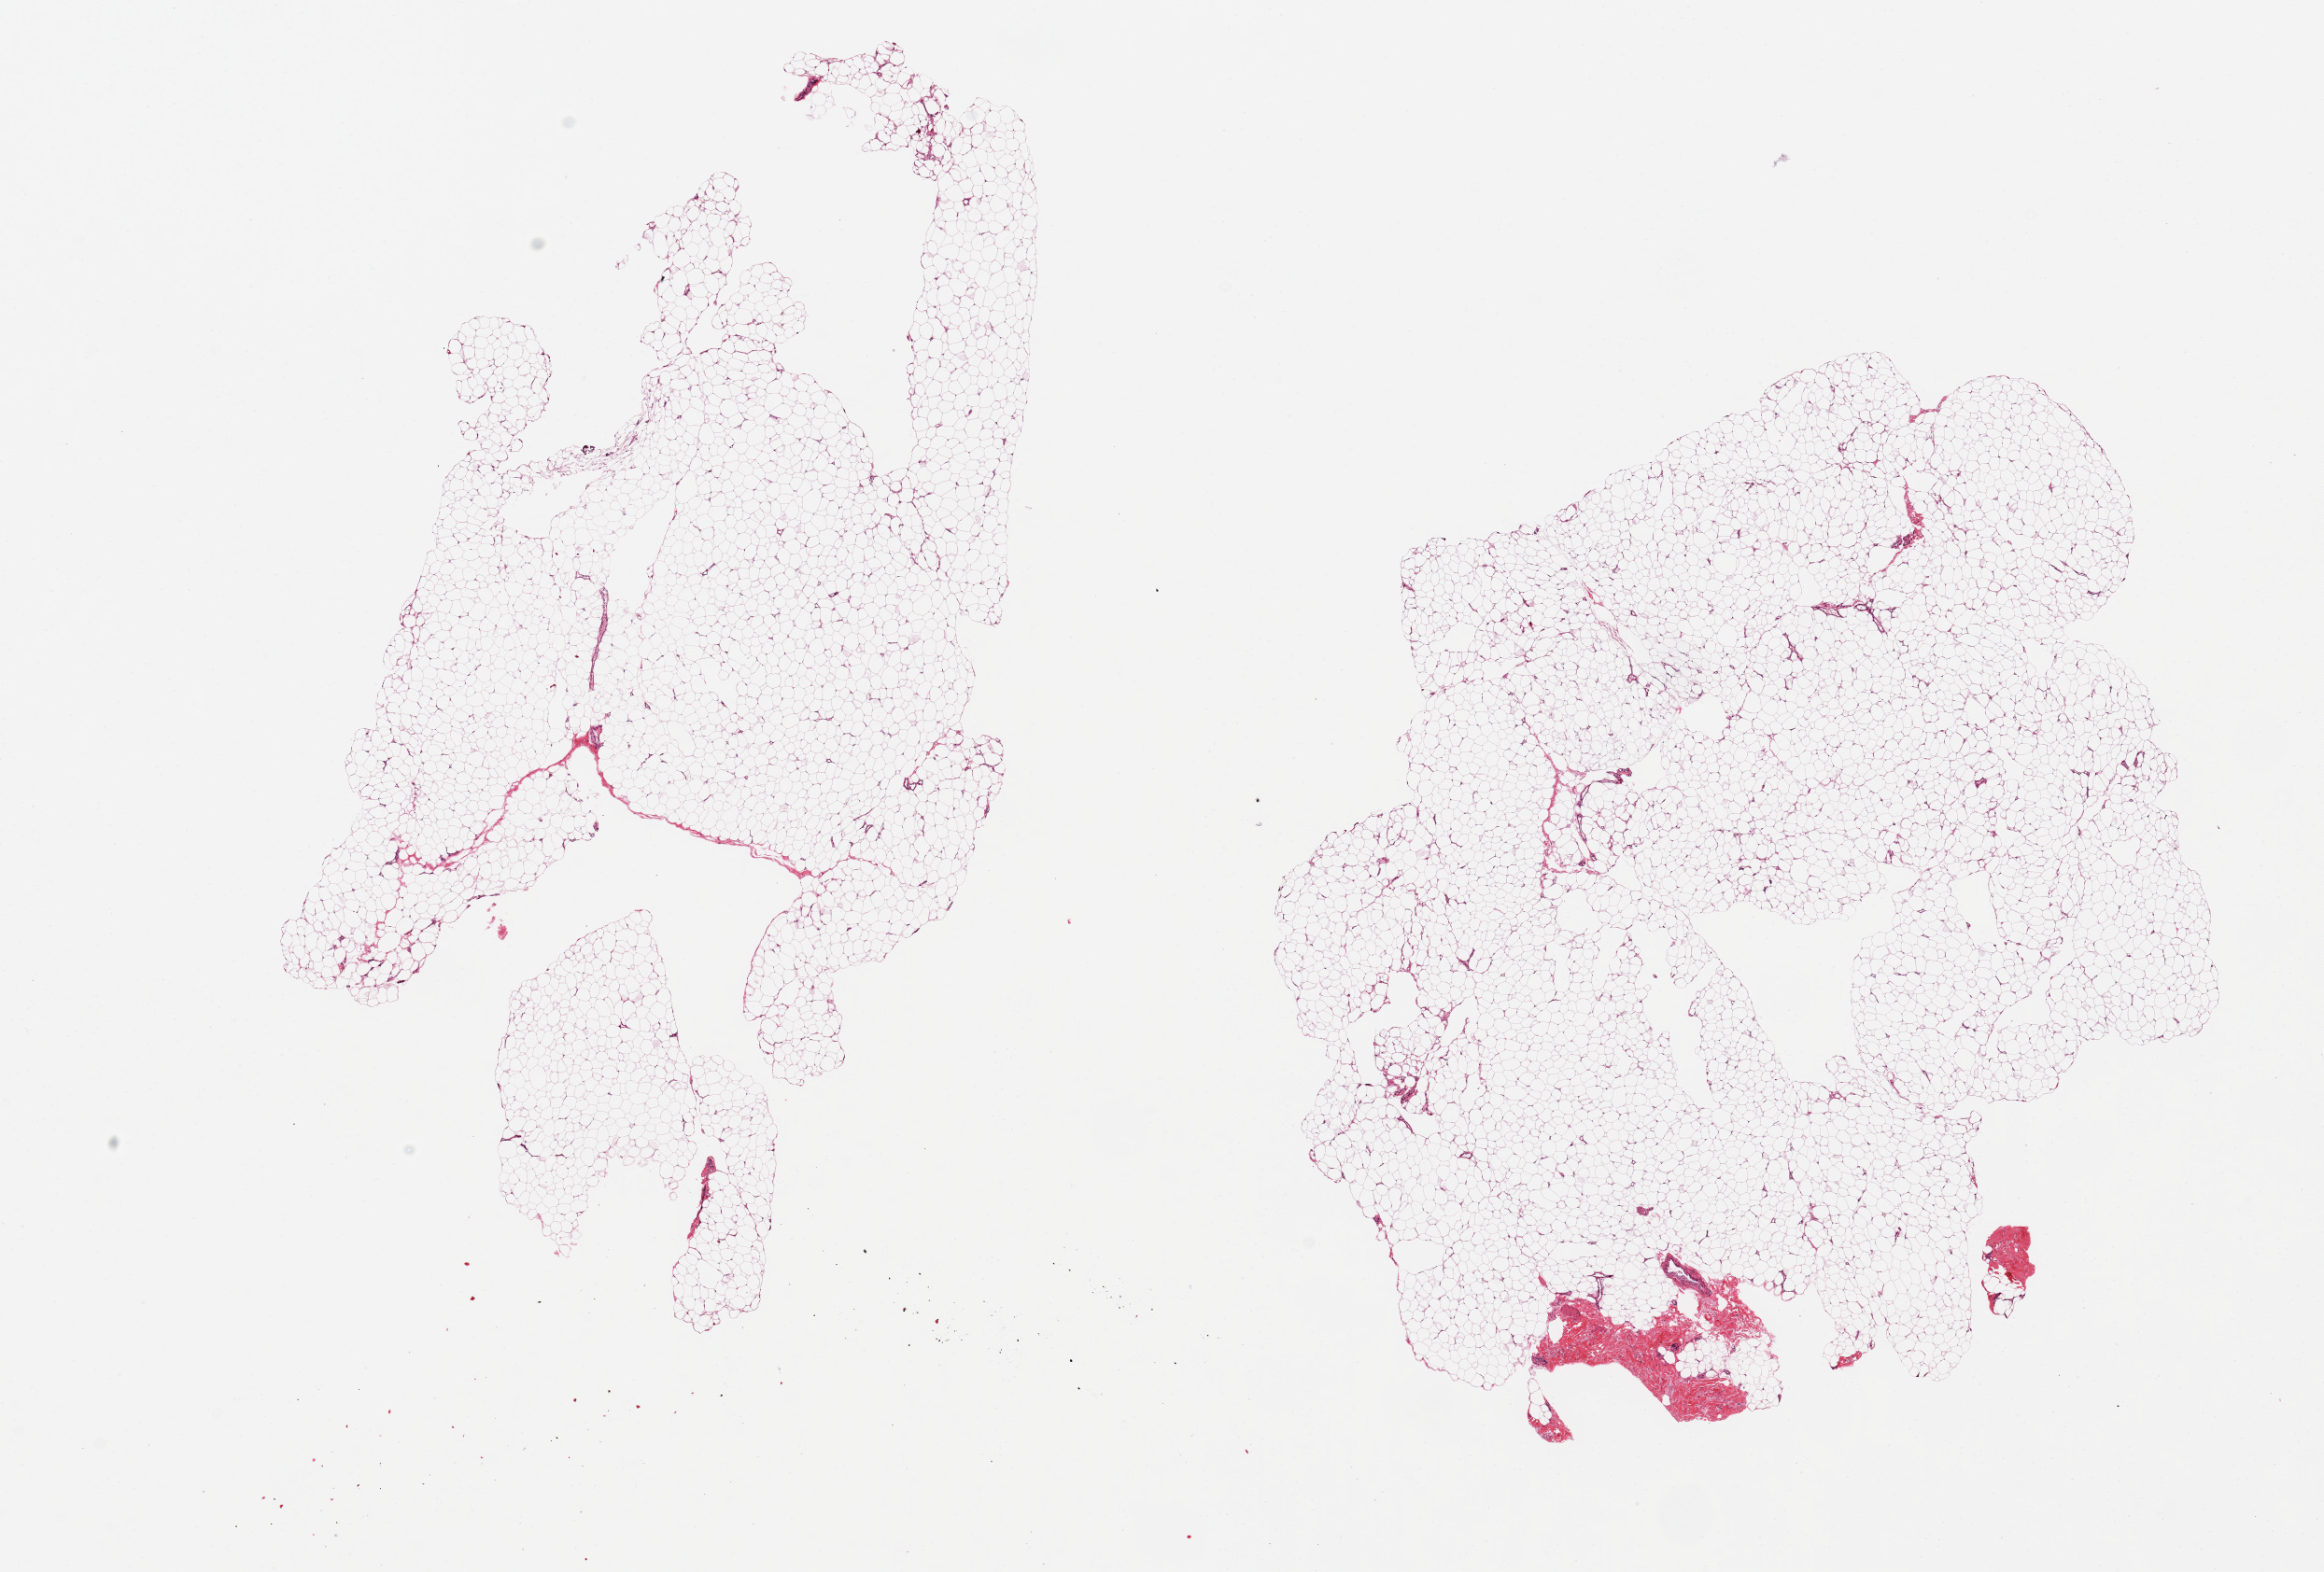
Hematoxylin and eosin (H&E) whole-slide image, shown as a low-resolution overview of the whole scanned area (about 19.7 x 13.3 mm); PAXgene-fixed paraffin-embedded (PFPE) section; section of adipose tissue (target tissue); tissue donor sample. Female donor.
Pathologist's review note for this sample: 2 ~9x6mm aliquots, fragmented.